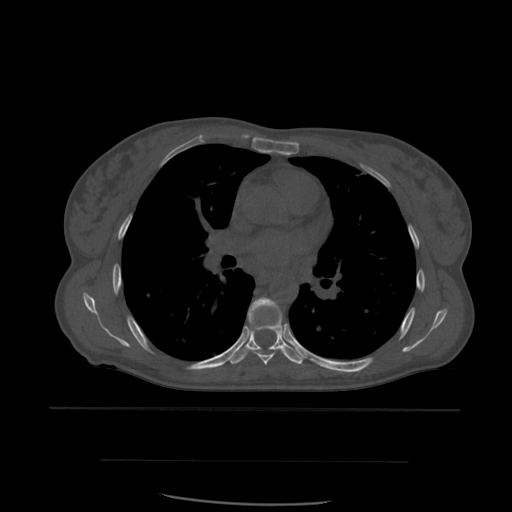
CT including the spine, one axial slice; position 383 of 574 along the scan axis; bone window (W 1800 / L 400 HU); 1.25 mm slice thickness; 512 × 512 image matrix, field of view 392 × 392 mm. Patient age 48 years. From the clinical record (not read from this slice): primary cancer: lung; vertebrae with lytic lesions (as recorded): T11.
Outlined on this slice (semi-automatically segmented with operator editing):
- T6 vertebra: bounding box [x1, y1, x2, y2] px = [248, 298, 285, 366]
- T7 vertebra: [230, 327, 304, 365]